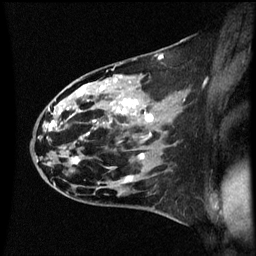
Breast MRI (dynamic contrast-enhanced), one sagittal slice; dynamic contrast-enhanced series, image 2 of 3 at this slice position (ordered by acquisition); 1.5 T; TE 4.2 ms, TR 8.9 ms; 256 × 256 image matrix. Female patient, age 44 years. From the clinical record (not read from this slice): setting: breast cancer imaged before/during neoadjuvant chemotherapy; receptor status: HR-positive, HER2-negative.
Structures marked on this image (semi-automatically segmented with operator editing):
- analysis volume of interest (the breast-tissue region the enhancement analysis was run in; not a lesion): bounding box <43,78,153,189> (left, top, right, bottom; pixels)
- tumour enhancement mask (voxels above the 70 % enhancement threshold inside the analysis volume of interest): <46,90,153,181>